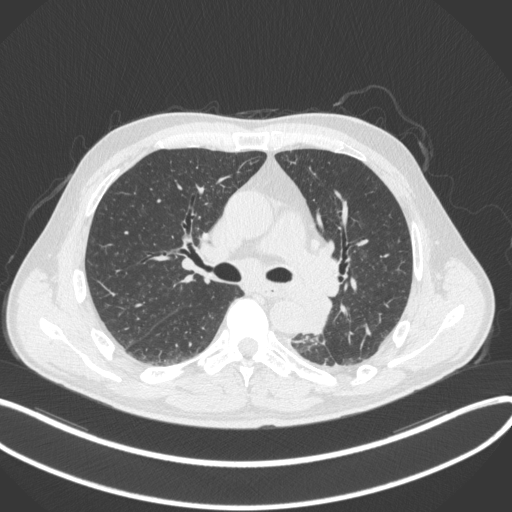
Chest CT, one axial slice; slice 210 of 328 in the series (ordered by position); reconstruction kernel B31f; lung window (W 1500 / L -600 HU); 1 mm slice thickness; 512 × 512 image matrix, field of view 400 × 400 mm. Patient: male, 59 years. Case-level facts recorded for this patient, not image findings: clinical TNM (as recorded): T2a N2 M0.
Annotated regions visible in this slice (bounding box drawn by a radiologist):
- lung tumour (recorded histology: squamous cell carcinoma): bounding box [x1, y1, x2, y2] px = [298, 288, 332, 336]